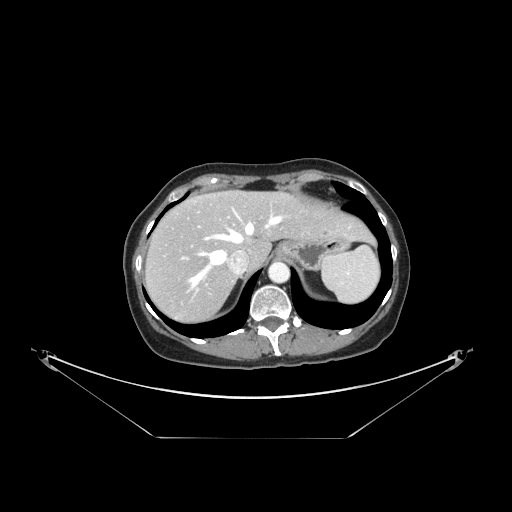
Contrast-enhanced abdominal CT, one axial slice. Slice 119 of 148 in the series (ordered by position). Reconstruction kernel STANDARD. Soft-tissue window (W 400 / L 40 HU). 512 × 512 image matrix, field of view 500 × 500 mm. Female patient, age 73 years. Case-level facts recorded for this patient, not image findings: diagnosis: colorectal cancer liver metastases, imaged before liver resection; multiple liver metastases: no; largest metastasis: 1 cm; disease in both lobes: no.
Outlined on this slice (outlined manually by an expert reader):
- hepatic veins: bounding box <189,209,284,287> (left, top, right, bottom; pixels)
- liver: <147,192,371,320>
- planned liver remnant (the part of the liver to remain after resection): <172,192,369,265>